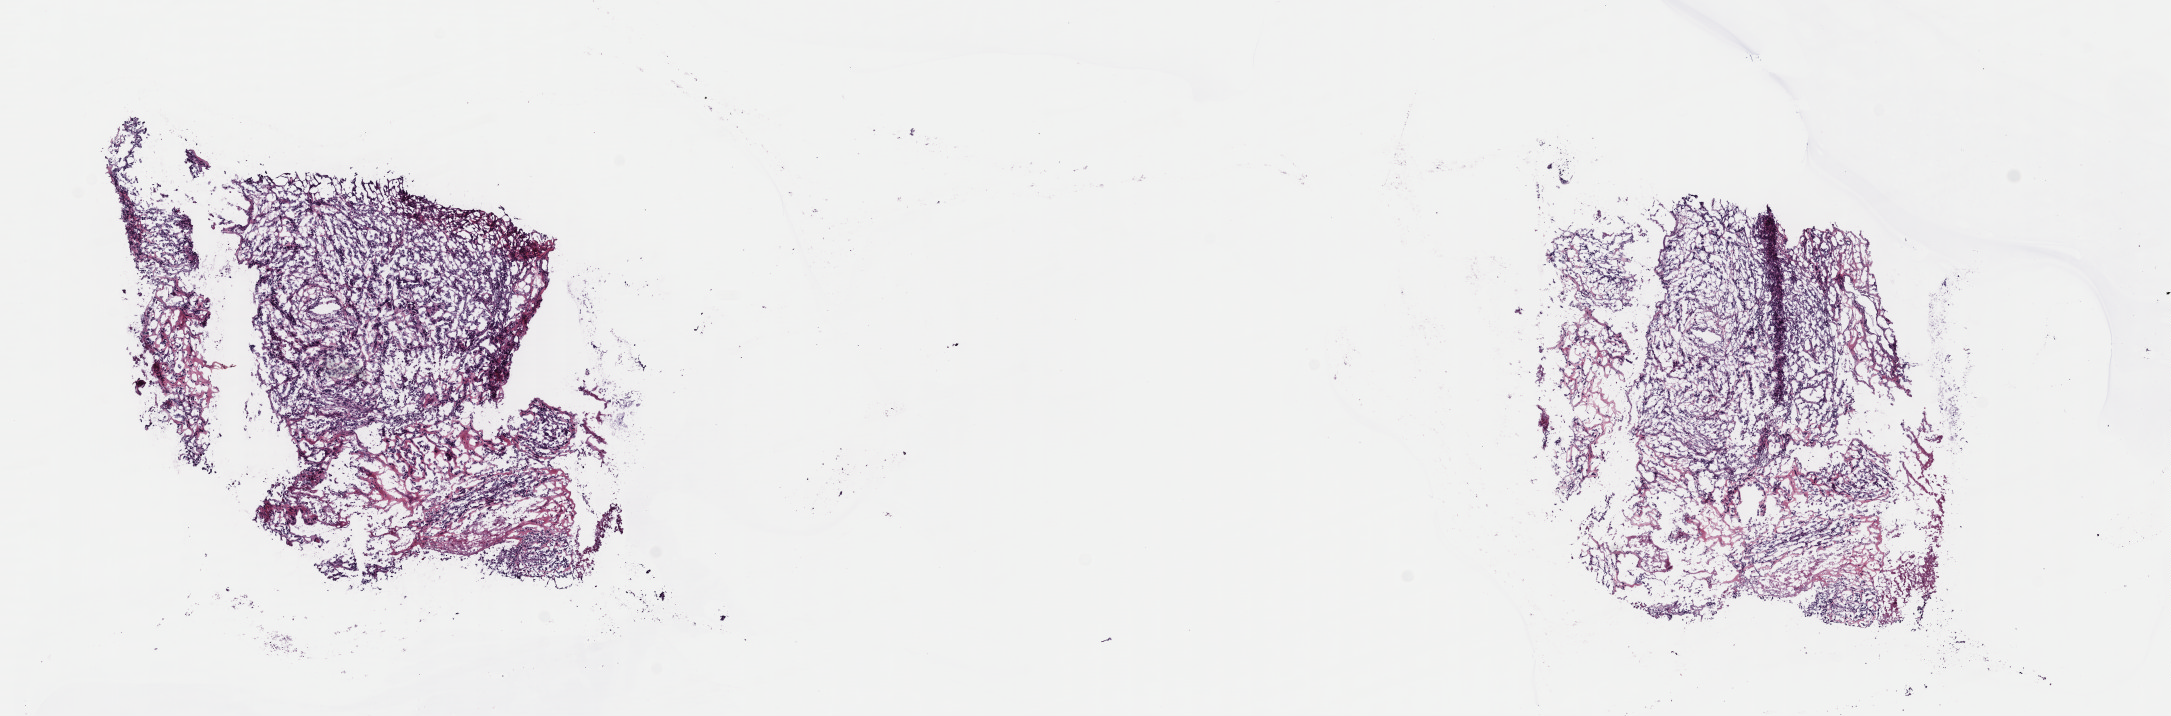
Whole-slide histology image, H&E-stained — low-resolution overview of the scanned area, about 17.1 x 5.6 mm (slide scanned at 40x); frozen section from the top of the tissue portion; primary tumour sample from the uterus. Patient: female, age at initial diagnosis 69 years. Slide review estimates, as recorded: tumour cells 80%, tumour nuclei 90%, normal cells 0%, stromal cells 10%, necrosis 10%. Infiltration values recorded for this section: lymphocyte infiltration 0%, monocyte infiltration 0%, neutrophil infiltration 0%.
Histologic diagnosis: Mullerian mixed tumor. FIGO stage: IVB.